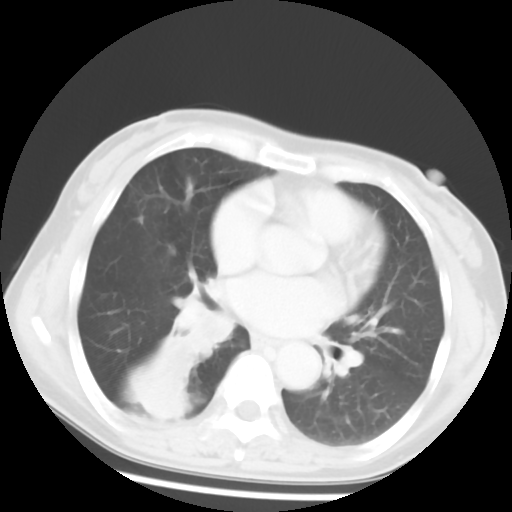
Chest CT, one axial slice; position 27 of 52 along the scan axis; lung window (W 1500 / L -600 HU); 5 mm slice thickness; 512 × 512 image matrix, field of view 297 × 297 mm. Patient: female, 54 years. Case-level facts recorded for this patient, not image findings: clinical TNM (as recorded): T1c N0 M0; histopathological grade: G1-2.
Outlined on this slice (bounding box drawn by a radiologist):
- lung tumour (recorded histology: squamous cell carcinoma): bounding box <164,286,228,369> (left, top, right, bottom; pixels)